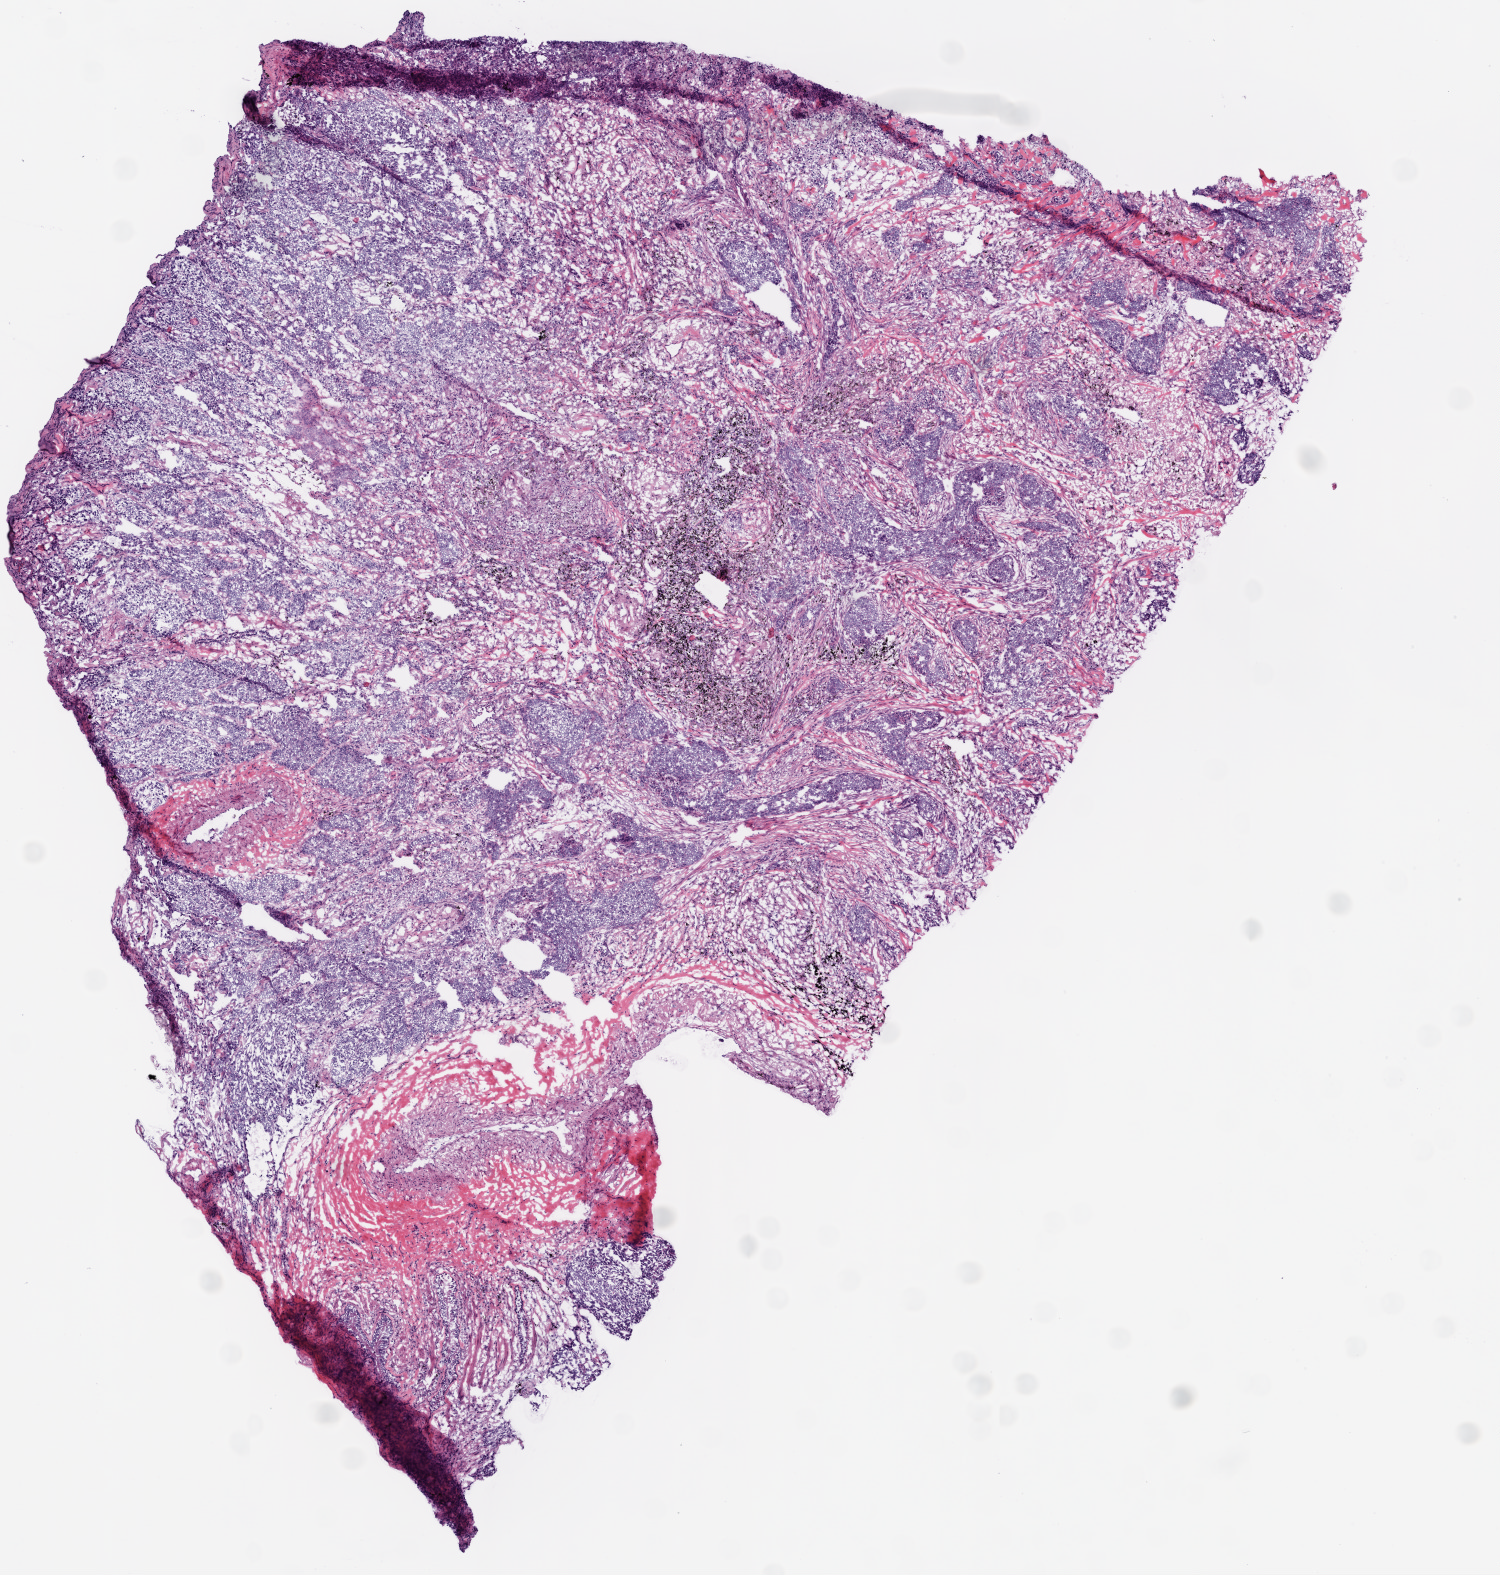
Whole-slide histology image, Hematoxylin and eosin (H&E) stained — a low-resolution overview of the entire scanned area, about 6.0 x 6.3 mm (acquisition: 20x scan); frozen section from the top of the tissue portion; sample: primary tumour, lung. Male patient; age at initial diagnosis 74 years. Pathologist review of this section (percent, as recorded): tumour cells 70%, tumour nuclei 80%, normal cells 0%, stromal cells 25%, necrosis 5%.
- TNM: T1 N0 M0
- AJCC pathologic stage: IA (6th edition)
- diagnosis: Basaloid squamous cell carcinoma (upper lobe, lung)